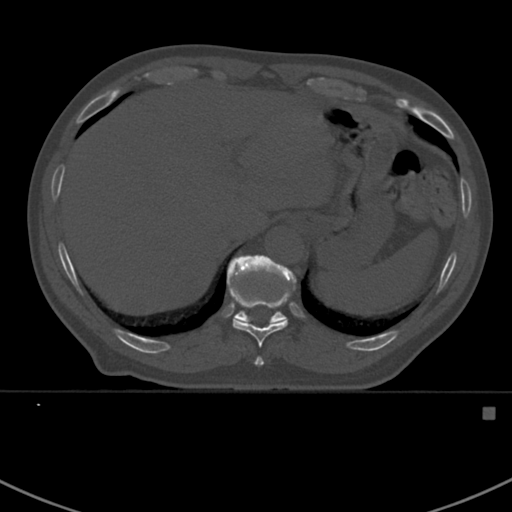
CT including the spine, one axial slice; position 361 of 412 along the scan axis; reconstruction kernel Br40s; 120 kVp; bone window (W 1800 / L 400 HU); 1.5 mm slice thickness; 512 × 512 image matrix, field of view 358 × 358 mm. Patient: male, 59 years. From the clinical record (not read from this slice): primary cancer: prostate.
Structures marked on this image (semi-automatically segmented with operator editing):
- T10 vertebra: bounding box (x1, y1, x2, y2) in pixels: (228, 285, 292, 366)
- T11 vertebra: (227, 255, 297, 323)